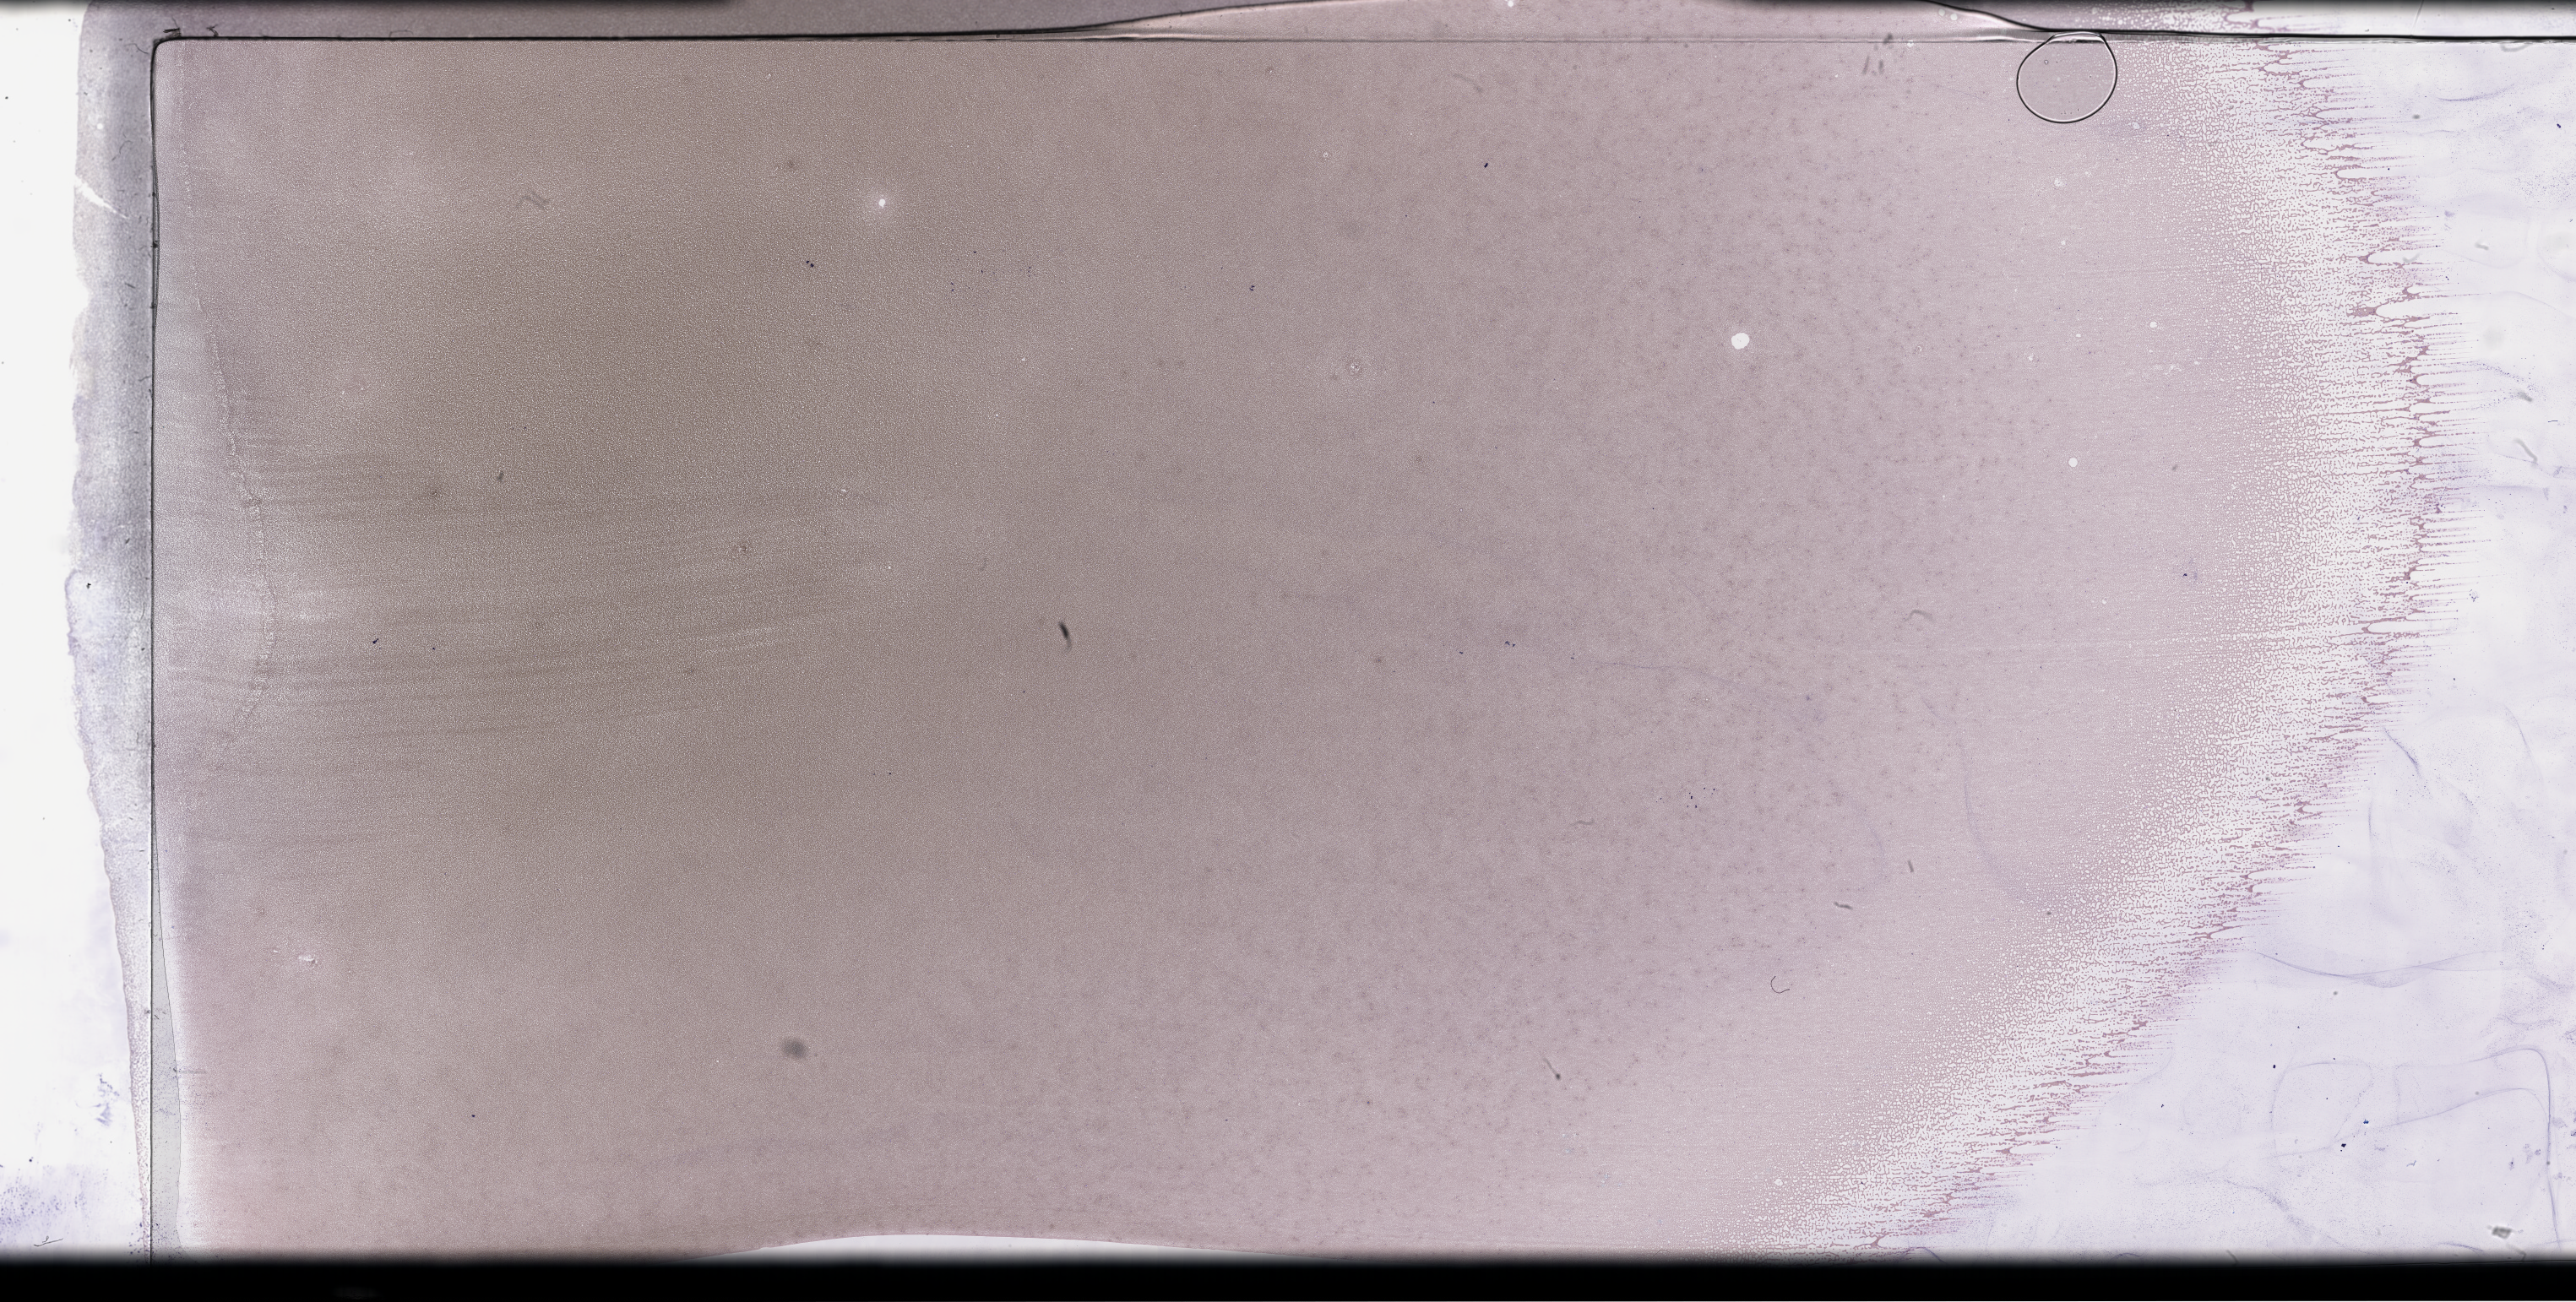
Whole-slide image of a whole blood smear, Wright–Giemsa stain — low-resolution overview of the scanned area, about 49.3 x 24.9 mm; smear from an EDTA sample; collected on treatment. Patient sex: male.
• from a patient with: Plasma Cell Myeloma